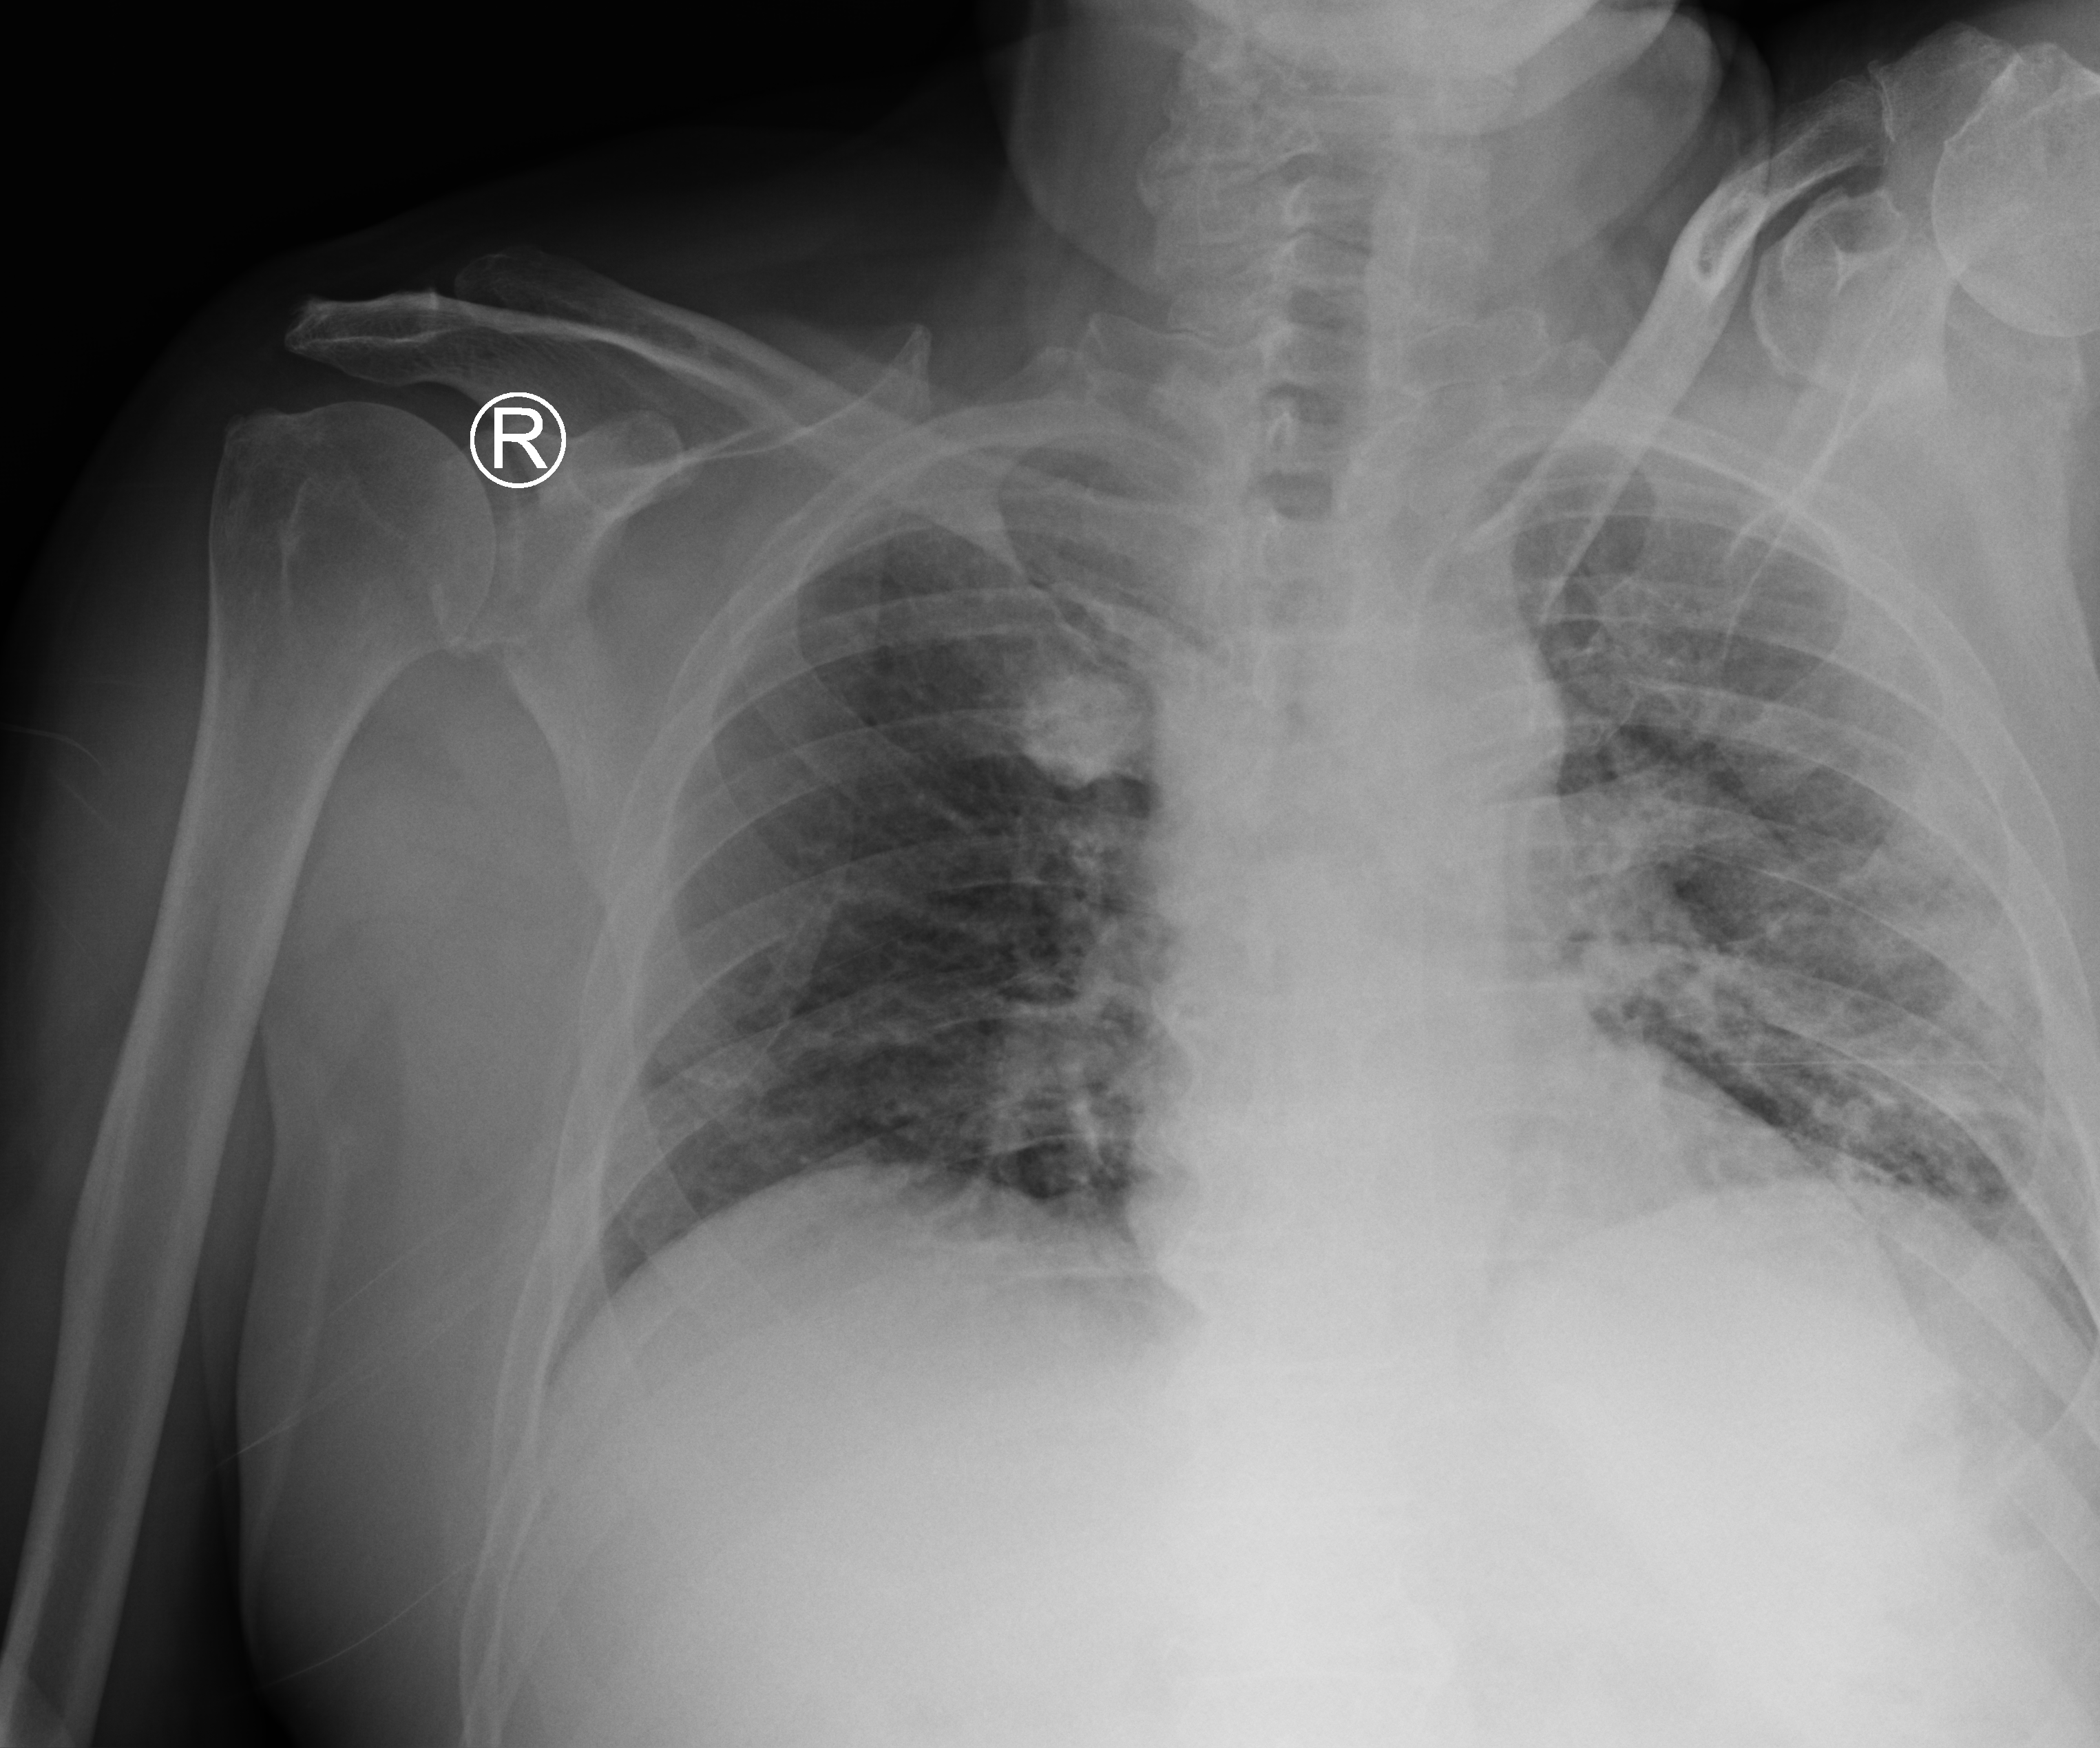
Portable chest radiograph; anteroposterior (AP) projection. Patient hospitalised with COVID-19; male, aged 75–90 years.
From the hospital-stay record, not from the radiograph (when in the stay this image was taken is not recorded): mechanically ventilated during this hospital stay: no; admitted to intensive care during this hospital stay: no.